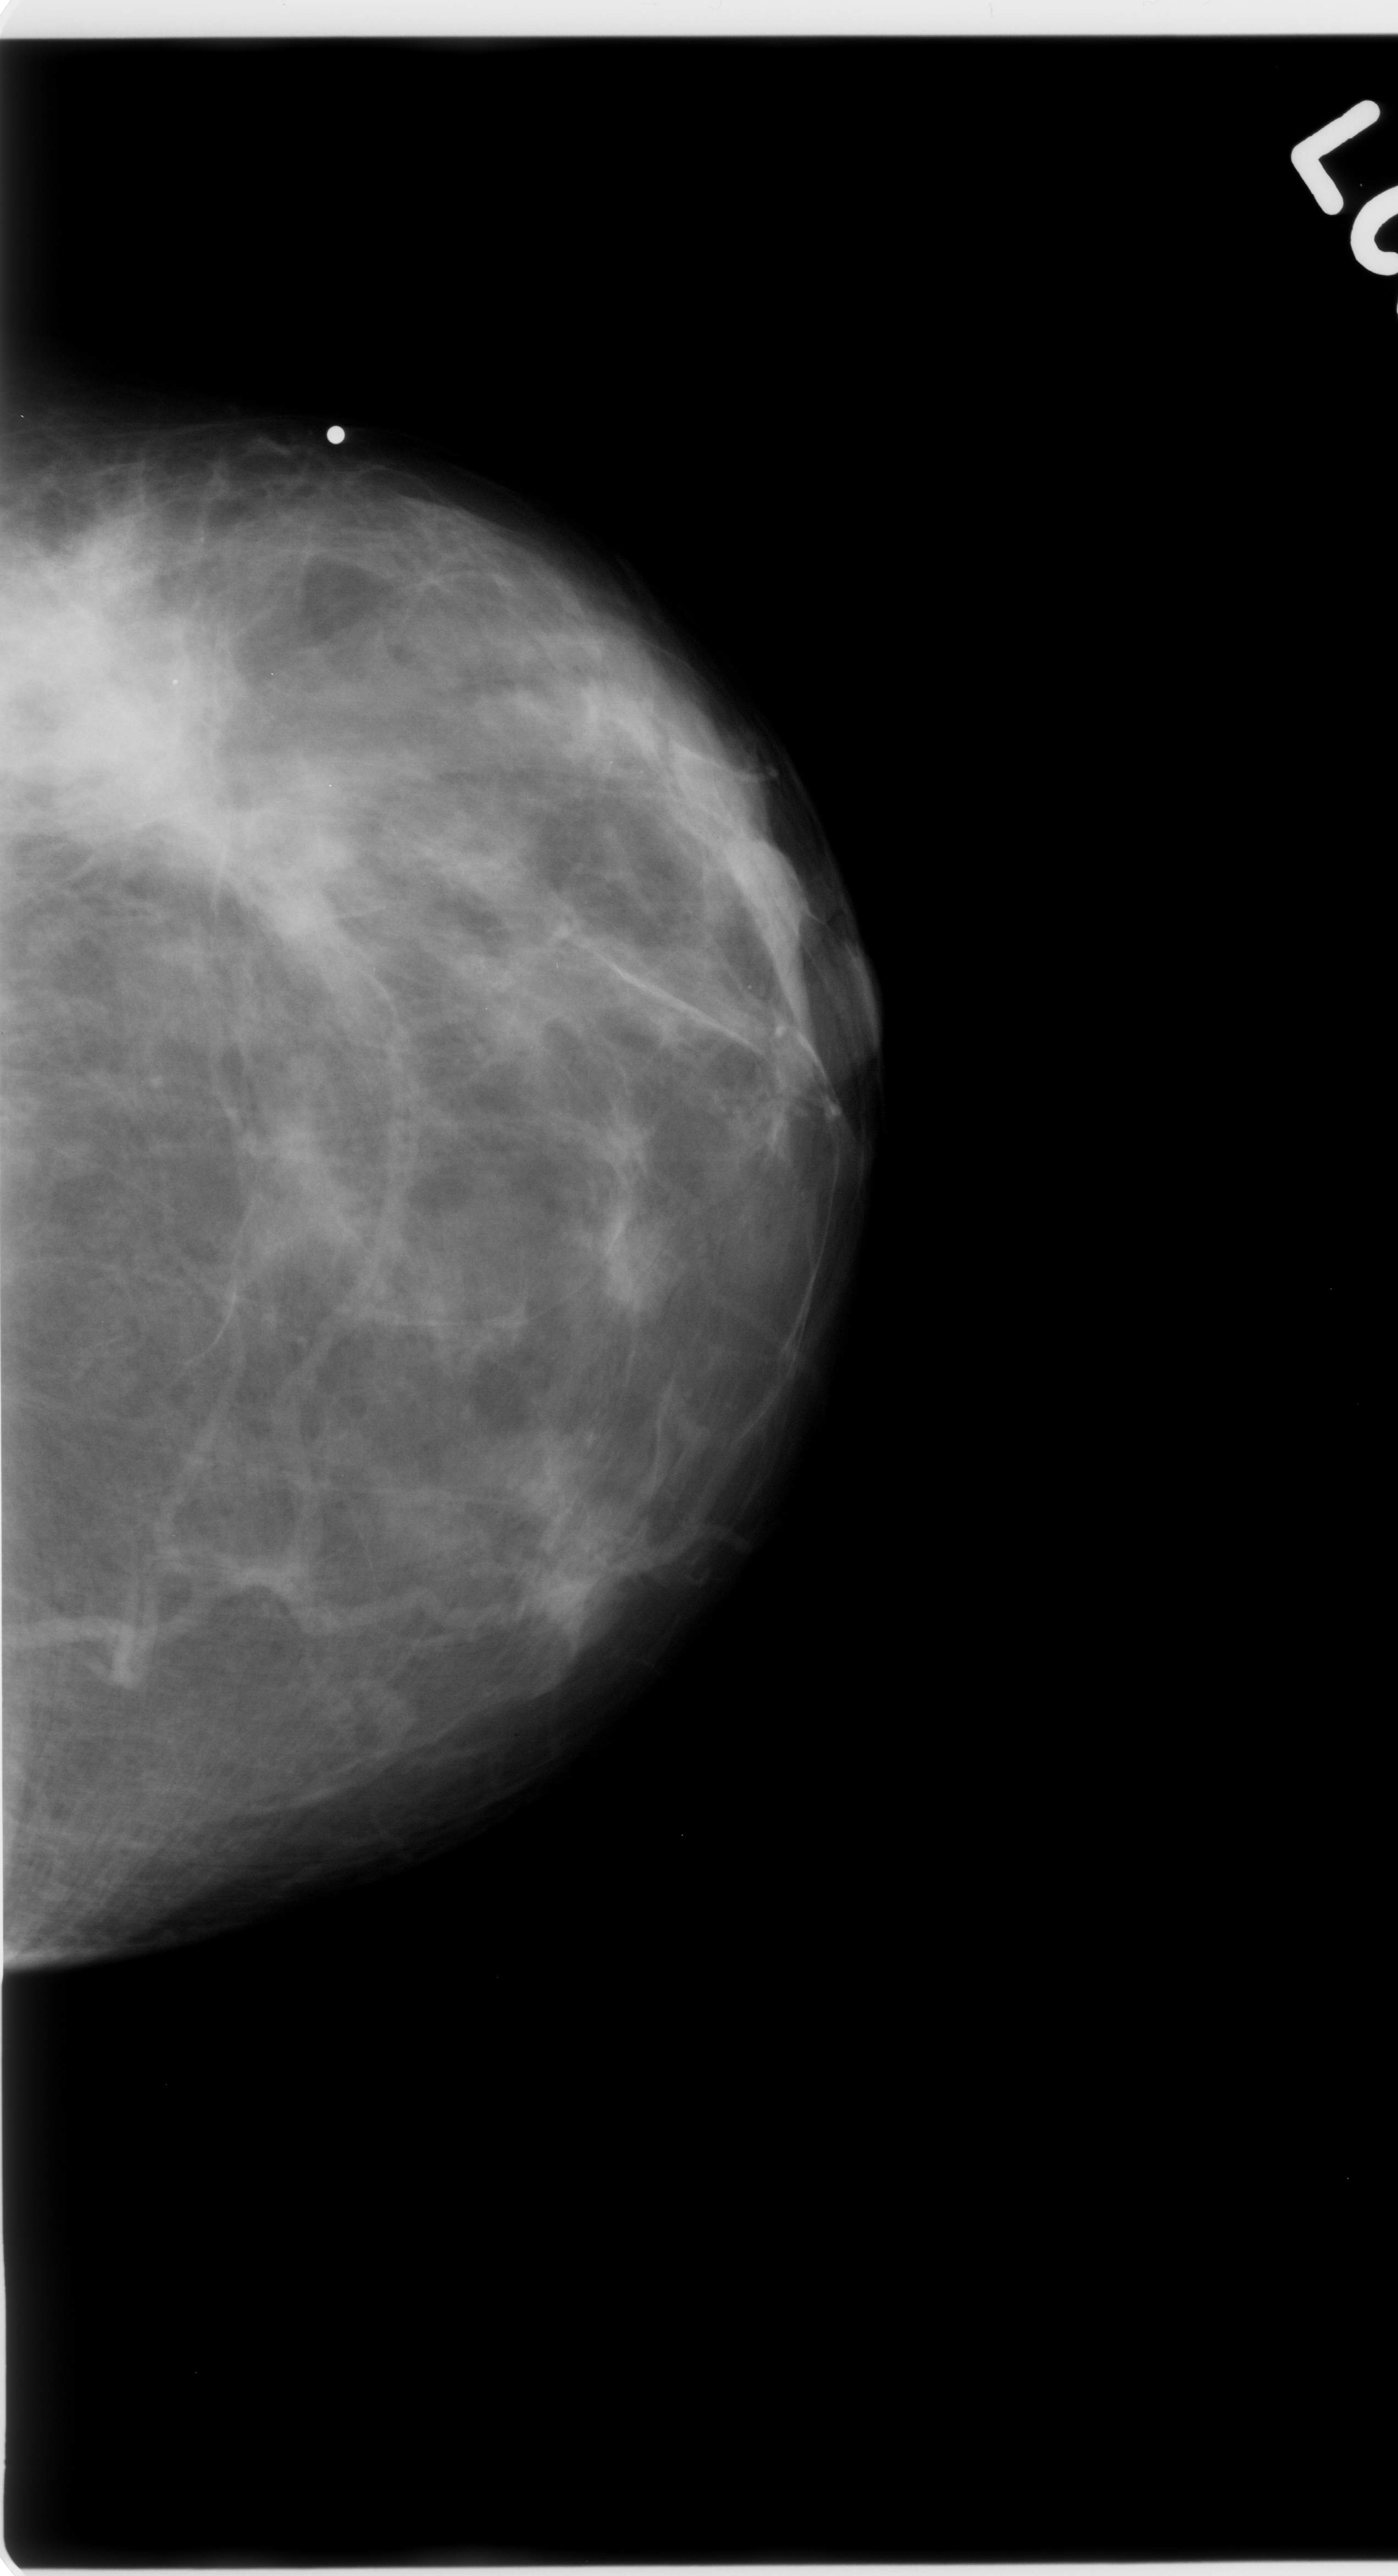
Digitized screen-film mammogram, left breast, CC view, BI-RADS breast density category 2 (scale 1–4).
- Abnormality record for this image: mass, shape irregular, margins ill defined; BI-RADS assessment category 5; pathology result (as recorded, not read from the image): malignant.